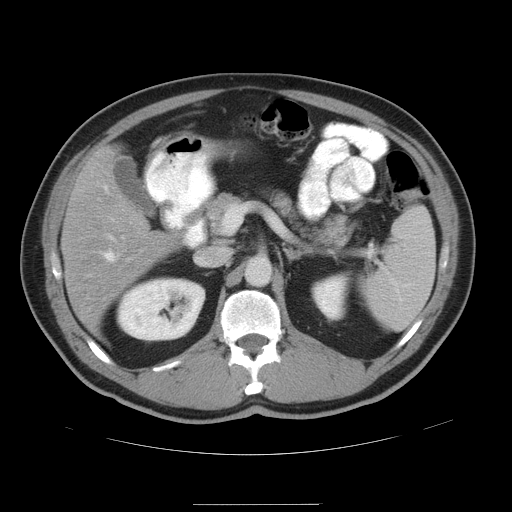
Contrast-enhanced abdominal CT, one axial slice; slice 25 of 47 in the series (ordered by position); 120 kVp; intravenous contrast given; soft-tissue window (W 400 / L 40 HU); 512 × 512 image matrix, field of view 420 × 420 mm. Male patient, age 61 years. Case-level facts recorded for this patient, not image findings: diagnosis: colorectal cancer liver metastases, imaged before liver resection; multiple liver metastases: no; largest metastasis: 1.2 cm.
Annotated regions visible in this slice (outlined manually by an expert reader):
- hepatic veins: box from (x=105, y=186) to (x=115, y=261) px
- liver: (x=63, y=147)–(x=179, y=334)
- planned liver remnant (the part of the liver to remain after resection): (x=67, y=147)–(x=179, y=333)